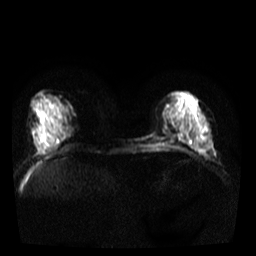
Breast MRI, one axial slice. Slice 15 of 40 in the series (ordered by position). Diffusion-weighted series; image 2 of 4 stored at this slice position (different b-values; order by instance number). 3 T. 256 × 256 image matrix. Female patient.
Outlined on this slice (expert manual segmentation):
- tumour on diffusion-weighted imaging: bounding box (x1, y1, x2, y2) in pixels: (200, 142, 212, 154)